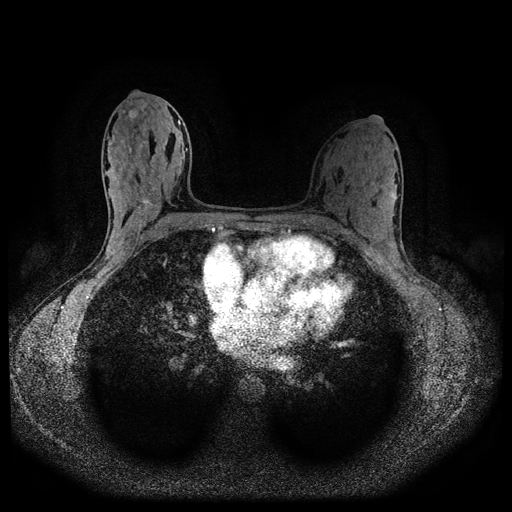
Breast MRI (dynamic contrast-enhanced, multi-phase), one axial slice. Slice 56 of 116 in the series (ordered by position). Dynamic contrast-enhanced series, time point 2 of 5 at this slice position (early post-contrast). 1.5 T. TE 2.7 ms, TR 5.4 ms. 2 mm slice thickness. 512 × 512 image matrix, field of view 330 × 330 mm. Patient: female, 32 years.
Outlined on this slice (semi-automatic segmentation, software-assisted and operator-edited):
- breast lesion (labelled benign in the annotation): bounding box [x1, y1, x2, y2] px = [128, 109, 143, 120]